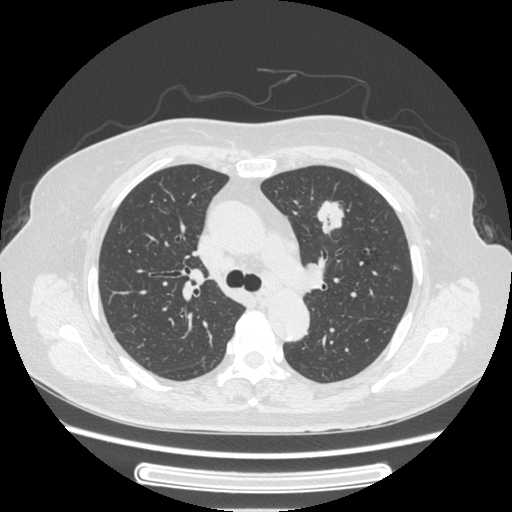
Chest CT, one axial slice. Slice 162 of 227 in the series (ordered by position). Reconstruction kernel STANDARD. Lung window (W 1500 / L -600 HU). 1.25 mm slice thickness. 512 × 512 image matrix. Patient: female, 77 years. From the clinical record (not read from this slice): clinical TNM (as recorded): T1c N3 M0; histopathological grade: G2-3.
Structures marked on this image (bounding box drawn by a radiologist):
- lung tumour (recorded histology: adenocarcinoma): bounding box <311,194,355,247> (left, top, right, bottom; pixels)